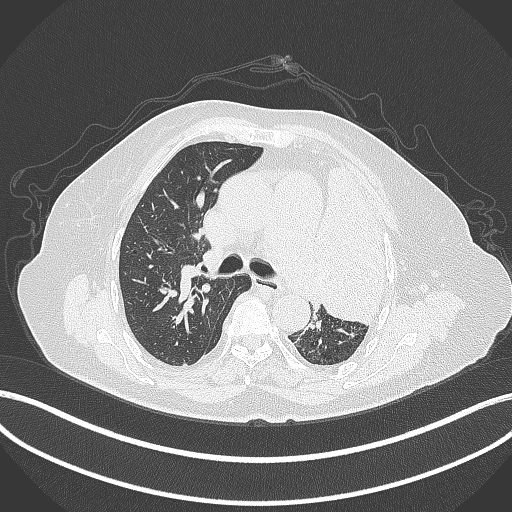
Chest CT, one axial slice. Reconstruction kernel B70f. 120 kVp. Lung window (W 1500 / L -600 HU). 512 × 512 image matrix, field of view 400 × 400 mm. Female patient, age 75 years. From the clinical record (not read from this slice): clinical TNM (as recorded): T3 N3 M1.
Structures marked on this image (rectangle marked by the reading radiologist):
- lung tumour (recorded histology: adenocarcinoma): bounding box (x1, y1, x2, y2) in pixels: (322, 153, 389, 331)